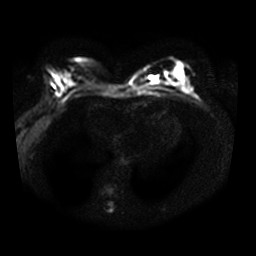
Breast MRI, one axial slice; position 17 of 34 along the scan axis; diffusion-weighted series; image 2 of 4 stored at this slice position (different b-values; order by instance number); 3 T; 5 mm slice thickness; 256 × 256 image matrix. Female patient.
Structures marked on this image (outlined manually by an expert reader):
- tumour on diffusion-weighted imaging: bounding box <152,77,159,84> (left, top, right, bottom; pixels)